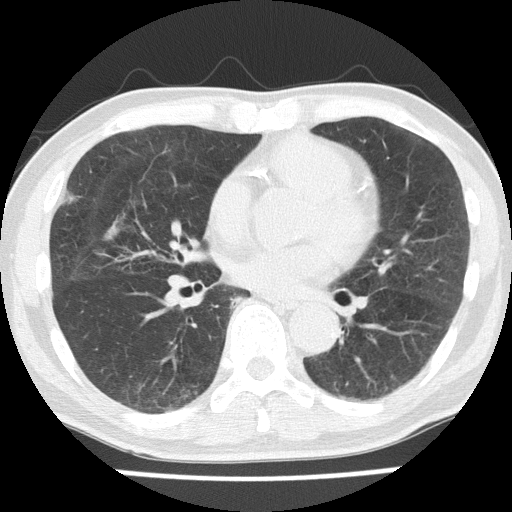
Axial slice from a low-dose chest CT screening exam; first (baseline) screen; lung window (W 1500 / L -600 HU); 120 kVp; slice 95 of 169 in the series; 512 × 512 image matrix. Male, age 68 years at enrolment. Current smoker at enrolment.
- Lesion marked by an expert reader, bounding box [x1, y1, x2, y2] px = [50, 183, 94, 218].
- Screening reader's record for this exam: no non-calcified nodule ≥4 mm recorded.
- Participant outcome: lung cancer diagnosed 386 days after this screen (after the second annual screen) — squamous cell carcinoma, NOS, right upper lobe, moderately differentiated (G2), stage IA (AJCC 6th edition), 10 mm at pathology.